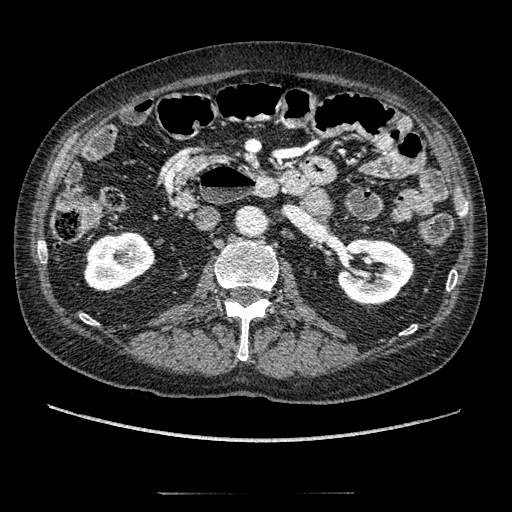
Contrast-enhanced abdominal CT, one axial slice. Slice 80 of 274 in the series (ordered by position). Intravenous contrast given. Soft-tissue window (W 400 / L 40 HU). 1.25 mm slice thickness. 512 × 512 image matrix. Male patient, age 69 years. From the clinical record (not read from this slice): diagnosis: adrenocortical carcinoma; tumour side: left adrenal; tumour size at pathology: 6.1 cm; Ki-67 index: 10 %; stage (as recorded): 3.
Annotated regions visible in this slice (semi-automatic segmentation, software-assisted and operator-edited):
- mass: box from (x=306, y=190) to (x=332, y=217) px